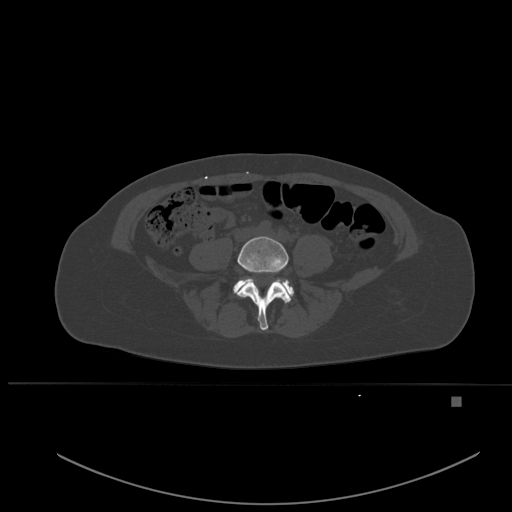
CT including the spine, one axial slice. Position 167 of 651 along the scan axis. Bone window (W 1800 / L 400 HU). 1.5 mm slice thickness. 512 × 512 image matrix, field of view 443 × 443 mm. Patient: female, 49 years. From the clinical record (not read from this slice): primary cancer: breast; vertebrae with lytic lesions (as recorded): L3, T12, L4.
Outlined on this slice (semi-automatic segmentation, software-assisted and operator-edited):
- L4 vertebra: bounding box <237,236,291,330> (left, top, right, bottom; pixels)
- L5 vertebra: <233,278,294,298>